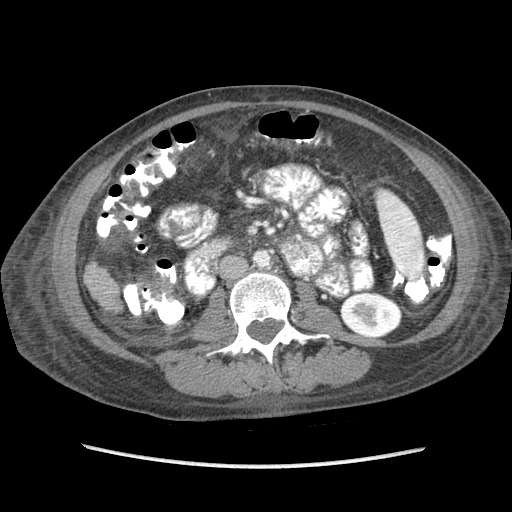
Contrast-enhanced abdominal CT (liver protocol), one axial slice; position 16 of 87 along the scan axis; reconstruction kernel STANDARD; soft-tissue window (W 400 / L 40 HU); 512 × 512 image matrix, field of view 340 × 340 mm. Case-level facts recorded for this patient, not image findings: diagnosis: hepatocellular carcinoma (patient treated with transarterial chemoembolisation; whether this scan precedes or follows treatment is not stated here); TNM stage (as recorded): Stage-IIIB; Child-Pugh class: A.
Outlined on this slice (semi-automatically segmented with operator editing):
- liver parenchyma outside the tumour (the mass and vessels are separate outlines, so this box may not span the whole liver): bounding box <86,263,106,292> (left, top, right, bottom; pixels)